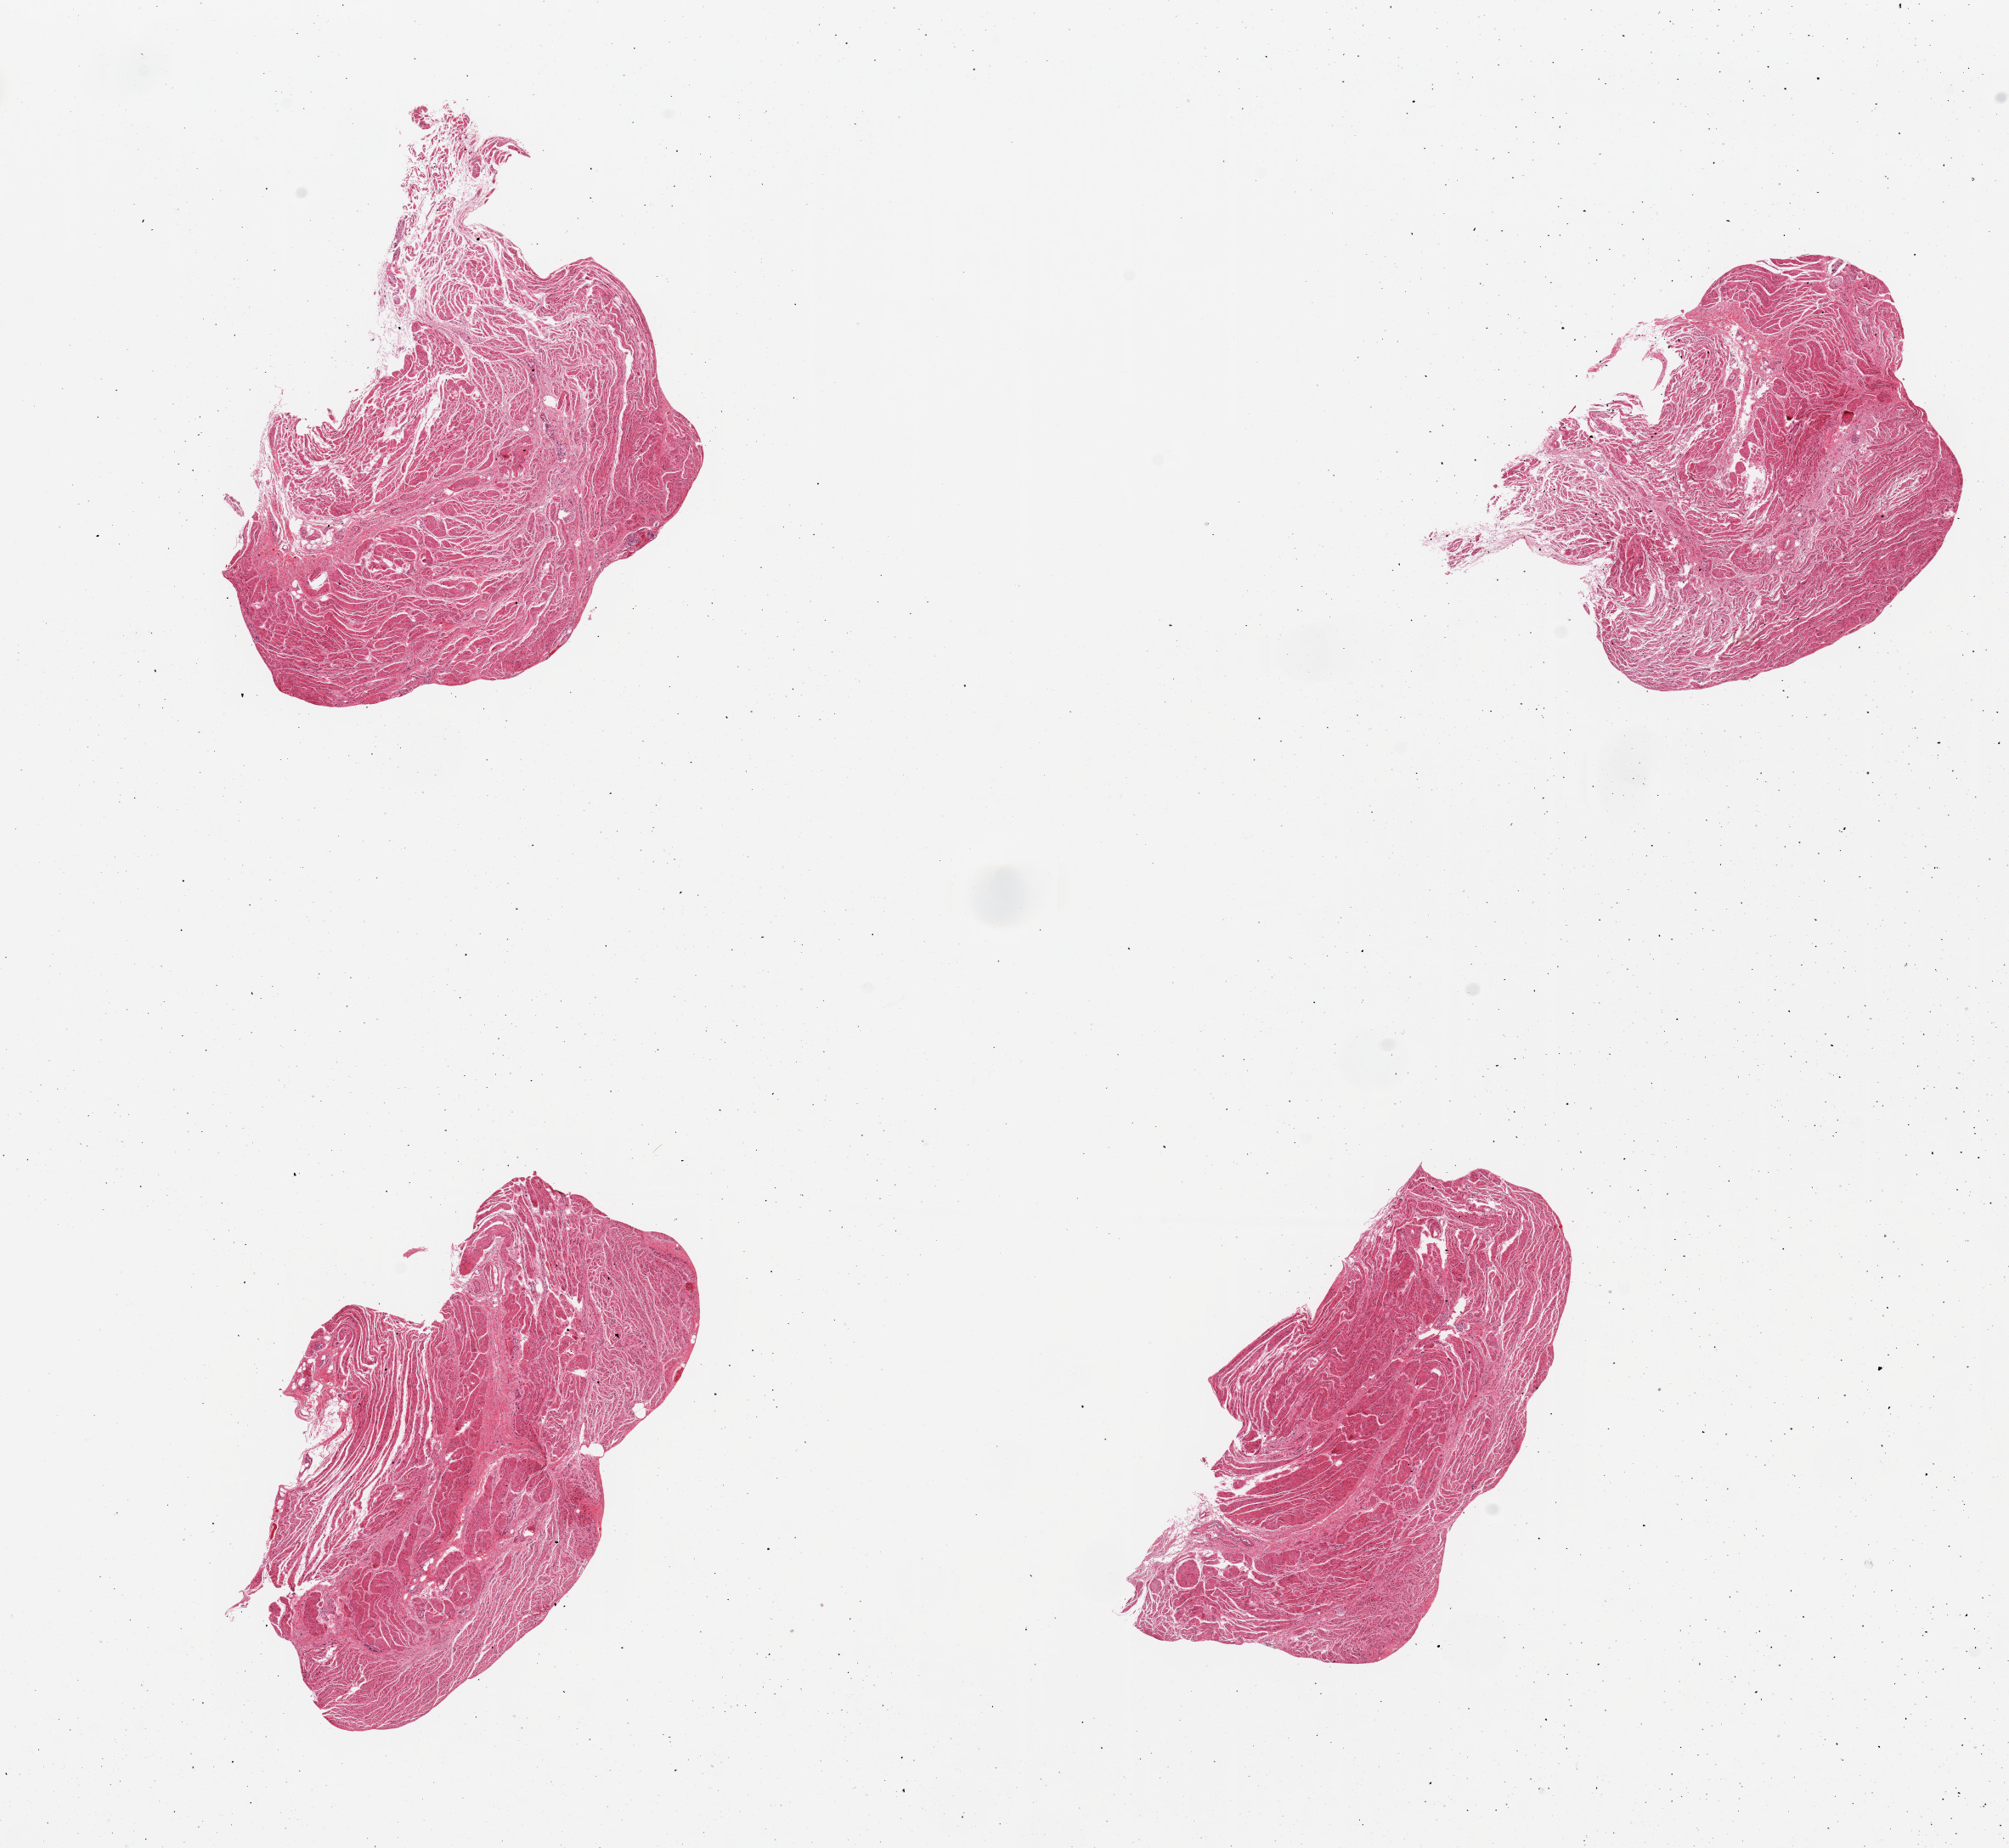
Digitized H&E-stained section, a low-resolution overview of the entire scanned area, about 18.7 x 17.2 mm, PAXgene-fixed, paraffin-embedded tissue, section of gastroesophageal junction (target tissue), donor tissue sample.
Review note (as recorded): 4 pieces.